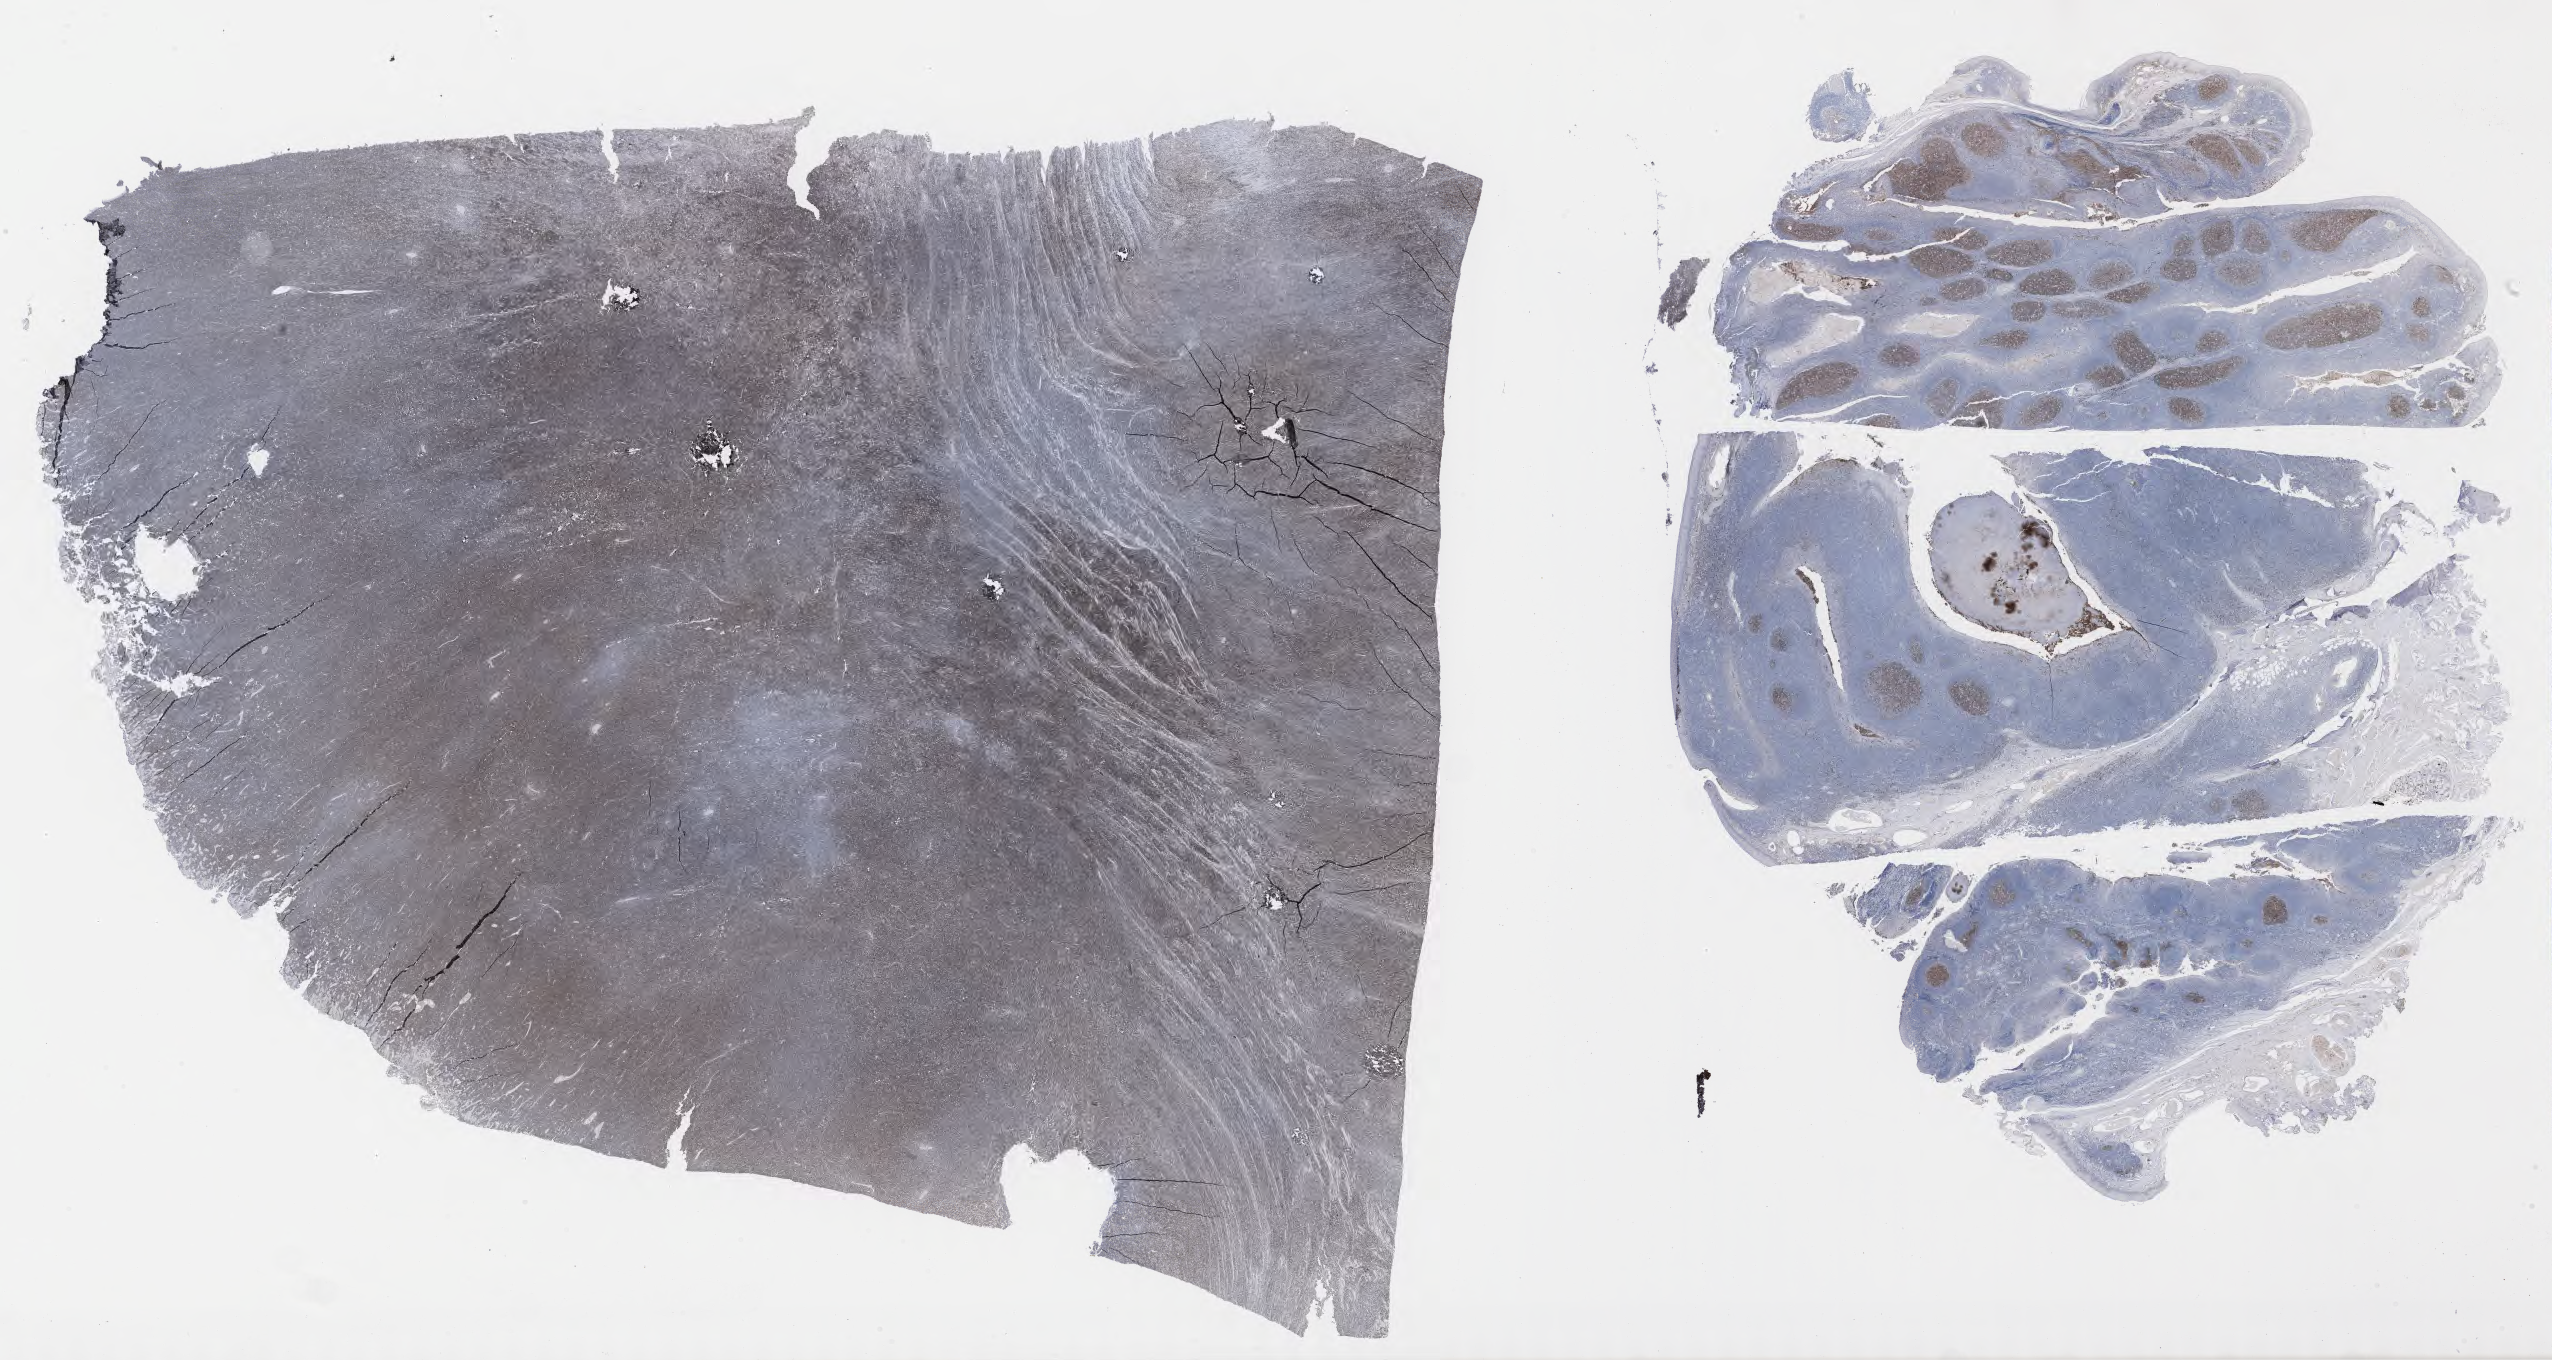
Immunohistochemistry (IHC) whole-slide image stained for CD10 — shown as a low-resolution overview of the whole scanned area (about 41.2 x 22.0 mm), specimen: tumor tissue. Male patient, aged 17.
* histologic diagnosis: Burkitt lymphoma, NOS